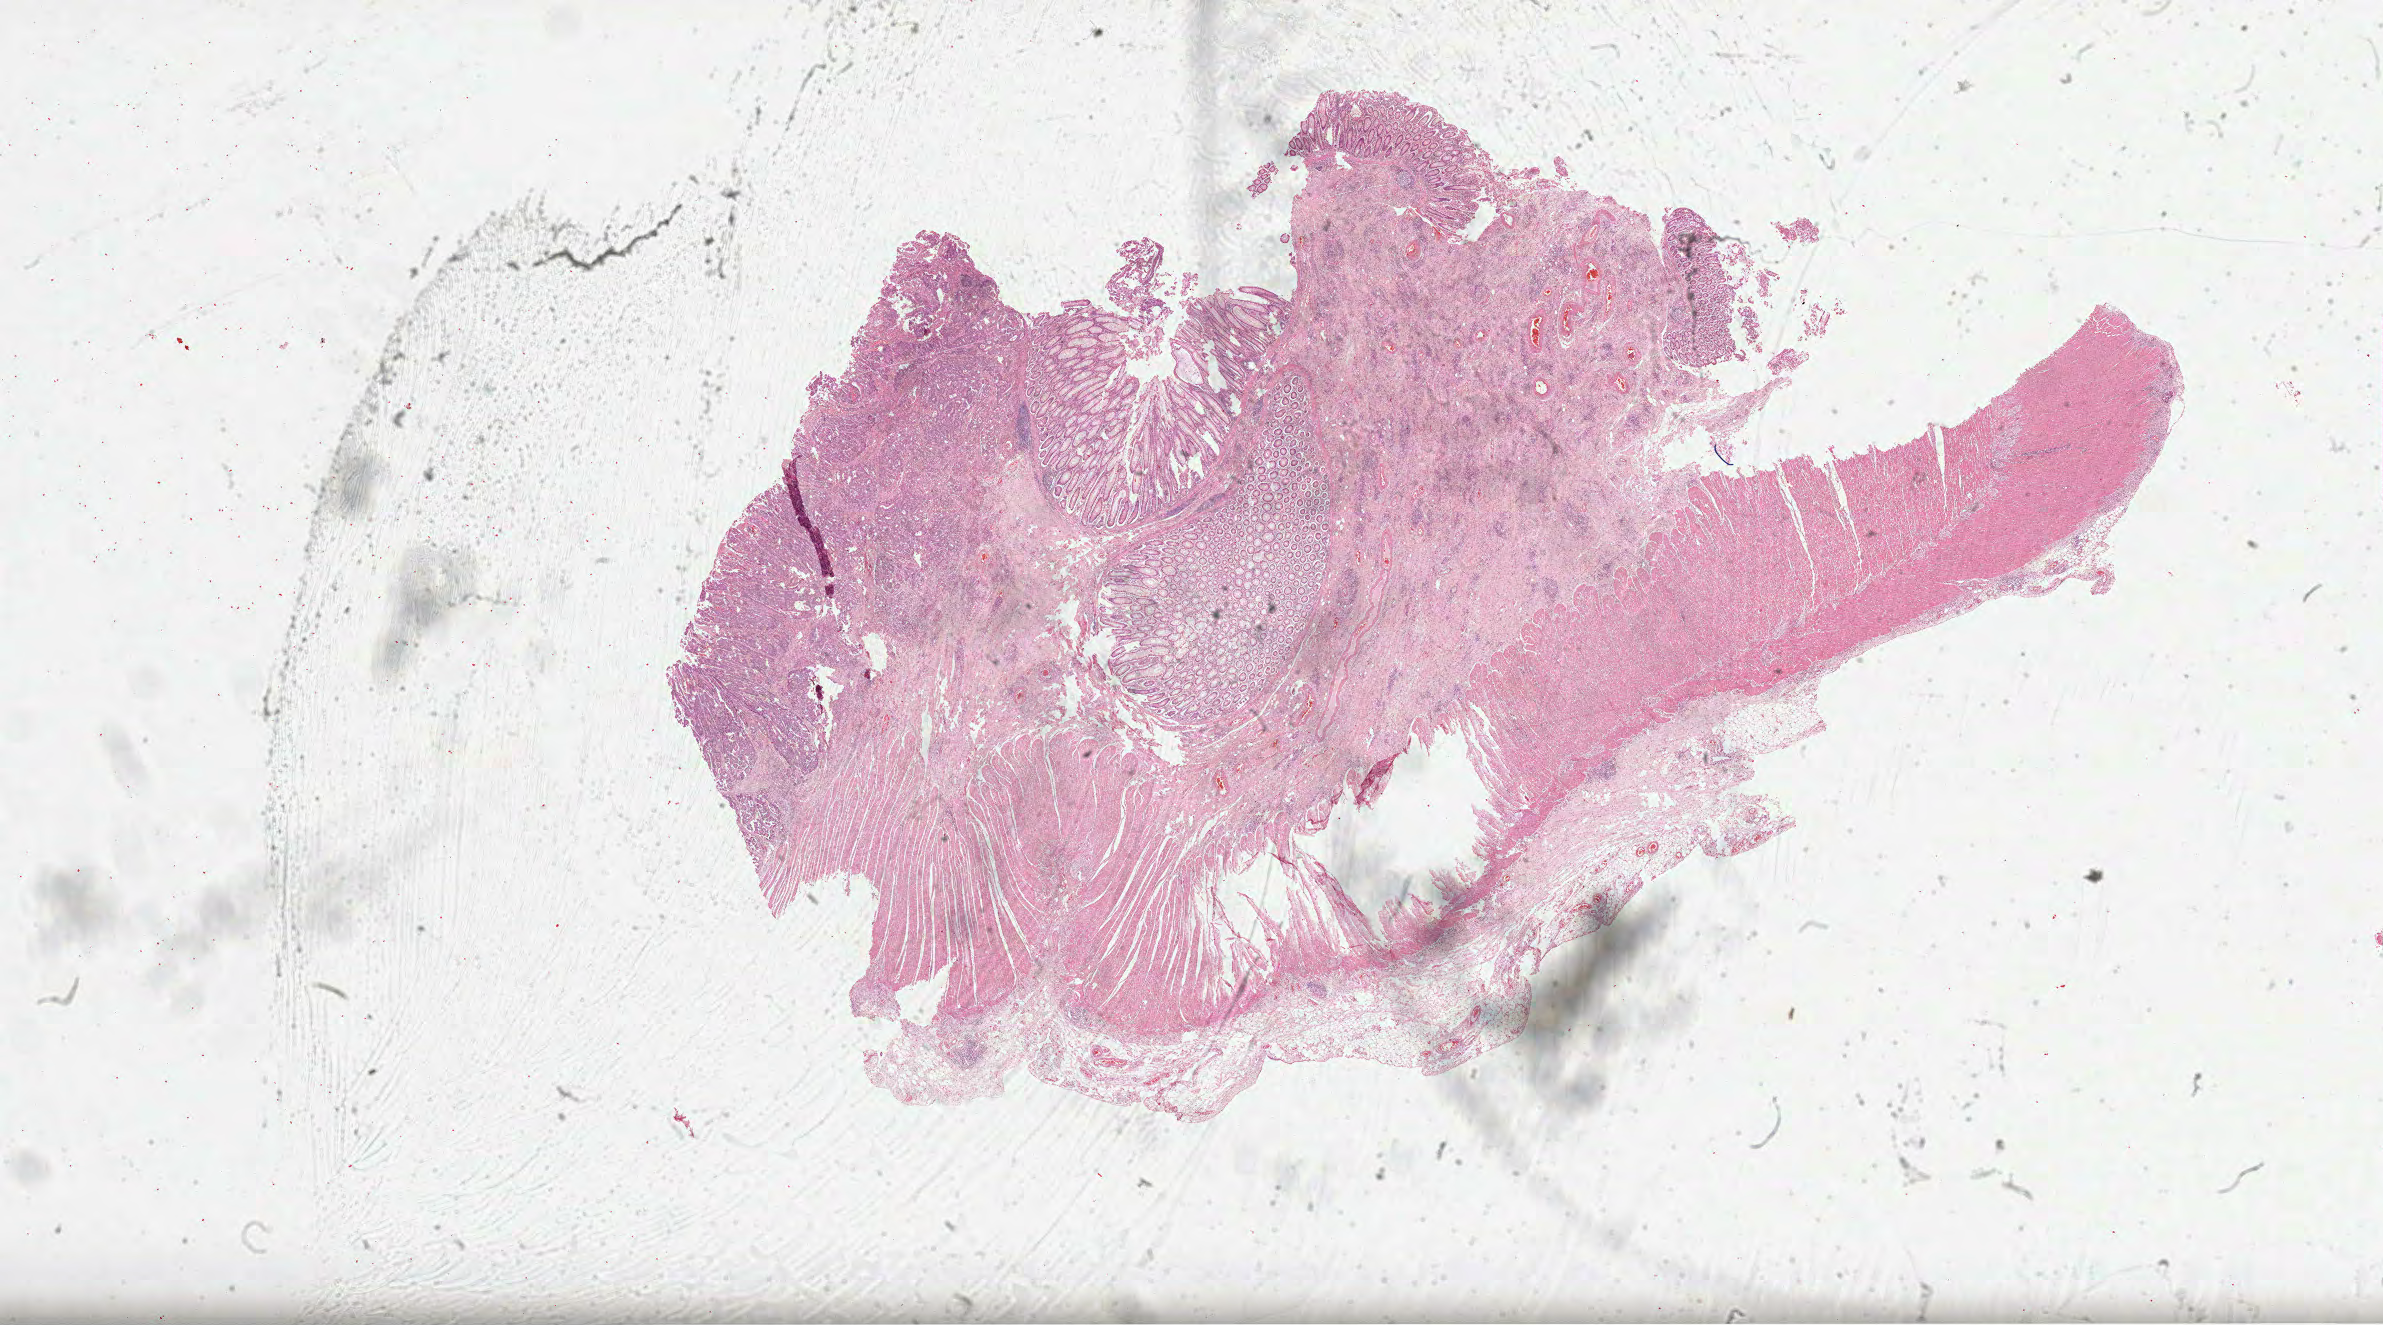
Digitized H&E-stained tissue section (whole slide), low-resolution overview of the scanned area, about 38.4 x 21.4 mm; formalin-fixed paraffin-embedded (FFPE) diagnostic section; primary tumour sample from the colon. Male patient; age at initial diagnosis 75 years.
* AJCC pathologic stage: IIA
* pathologic diagnosis: Adenocarcinoma, NOS
* lymph nodes positive (case pathology): 0 of 4 examined